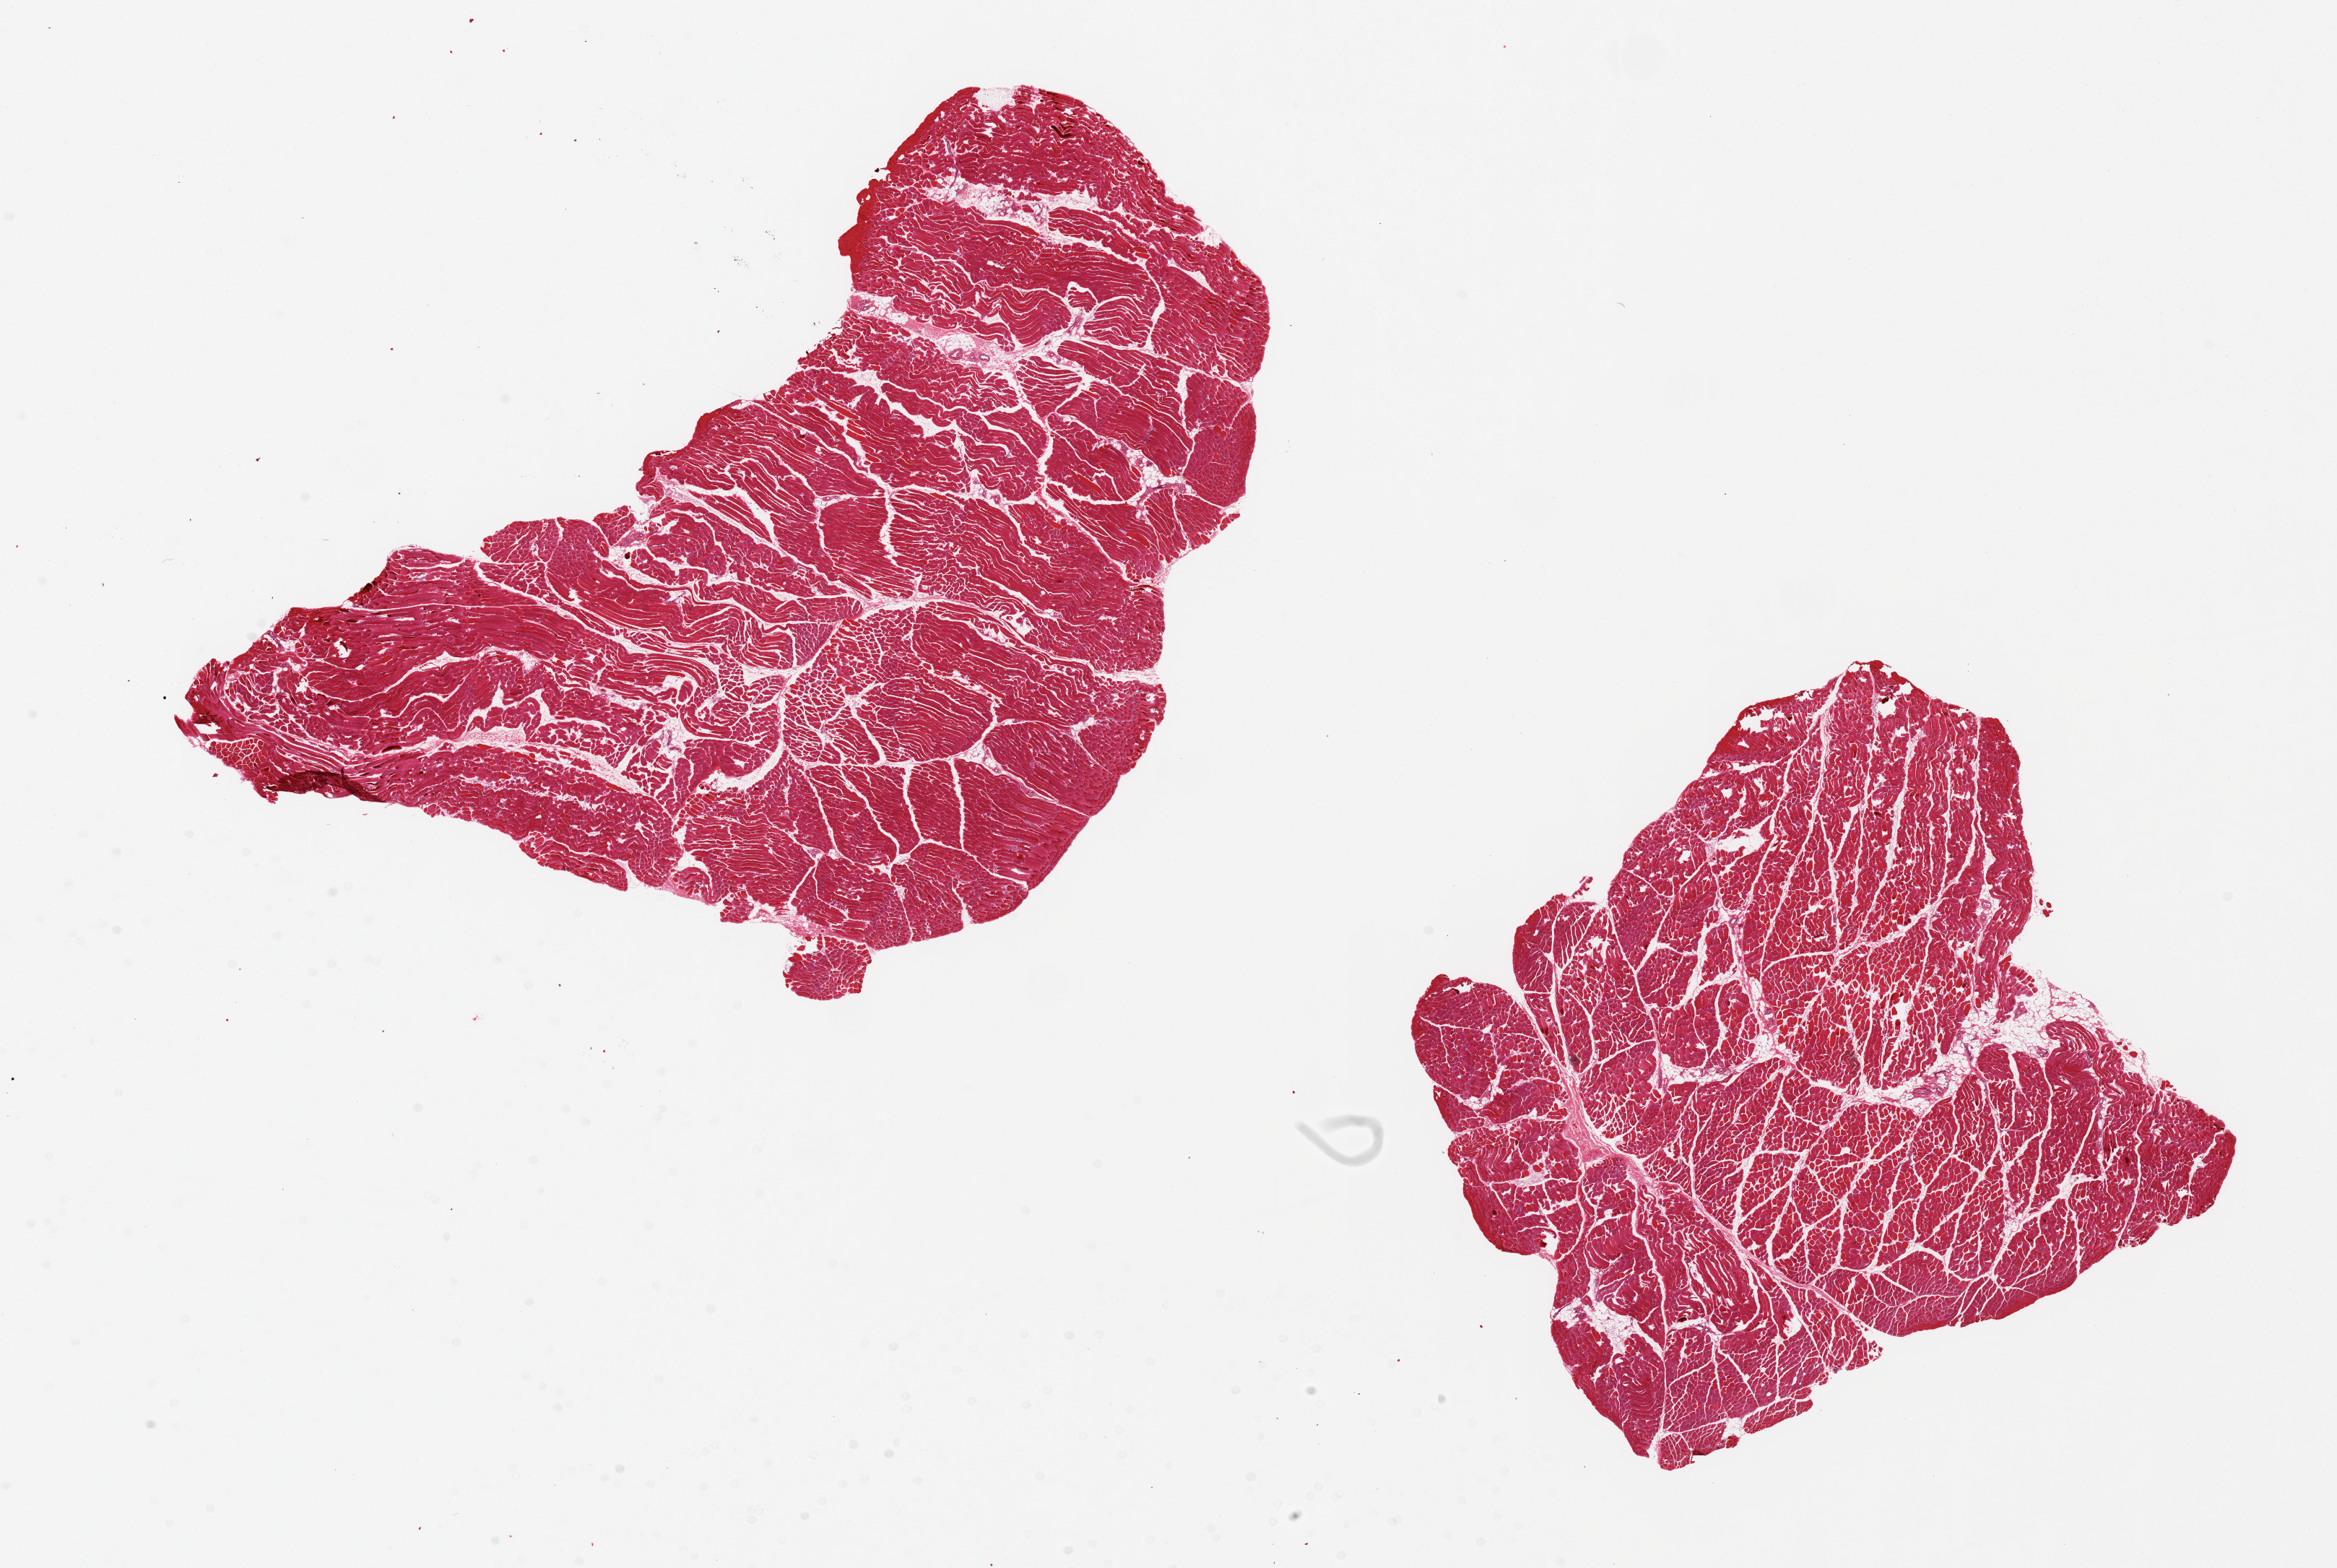
Digitized hematoxylin and eosin (H&E)-stained section — whole scanned area (about 25.6 x 17.2 mm, slide scanned at 20x) shown as a low-resolution overview, PAXgene-fixed paraffin-embedded (PFPE) section, target tissue: skeletal muscle, donor tissue sample. Female donor.
Pathologist's review note for this sample: 2 pieces 12x6 & 7x7 mm; minimal adipose.